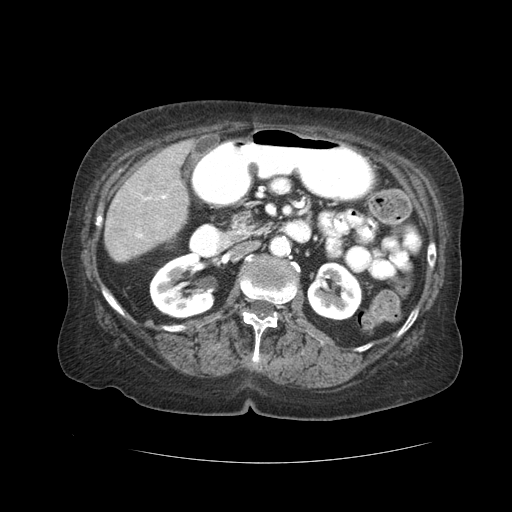
Contrast-enhanced abdominal CT (liver protocol), one axial slice; position 6 of 59 along the scan axis; reconstruction kernel STANDARD; 120 kVp; soft-tissue window (W 400 / L 40 HU); 2.5 mm slice thickness; 512 × 512 image matrix. Case-level facts recorded for this patient, not image findings: diagnosis: hepatocellular carcinoma (patient treated with transarterial chemoembolisation; whether this scan precedes or follows treatment is not stated here); TNM stage (as recorded): Stage-I; Child-Pugh class: A.
Structures marked on this image (semi-automatically segmented with operator editing):
- liver parenchyma outside the tumour (the mass and vessels are separate outlines, so this box may not span the whole liver): bounding box (x1, y1, x2, y2) in pixels: (104, 140, 196, 262)
- liver vessels: (135, 195, 166, 238)